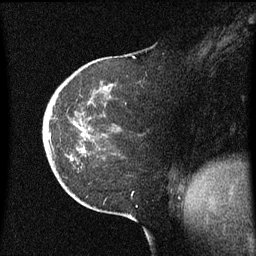
Breast MRI (dynamic contrast-enhanced), one sagittal slice. Slice 19 of 60 in the series (ordered by position). Dynamic contrast-enhanced series, image 2 of 3 at this slice position (ordered by acquisition). 1.5 T. TE 4.2 ms, TR 8.4 ms. 2 mm slice thickness. 256 × 256 image matrix. Female patient, age 38 years. From the clinical record (not read from this slice): setting: breast cancer imaged before/during neoadjuvant chemotherapy; receptor status: HER2-positive.
Outlined on this slice (semi-automatic segmentation, software-assisted and operator-edited):
- analysis volume of interest (the breast-tissue region the enhancement analysis was run in; not a lesion): bounding box (x1, y1, x2, y2) in pixels: (43, 54, 137, 185)
- tumour enhancement mask (voxels above the 70 % enhancement threshold inside the analysis volume of interest): (50, 134, 52, 137)